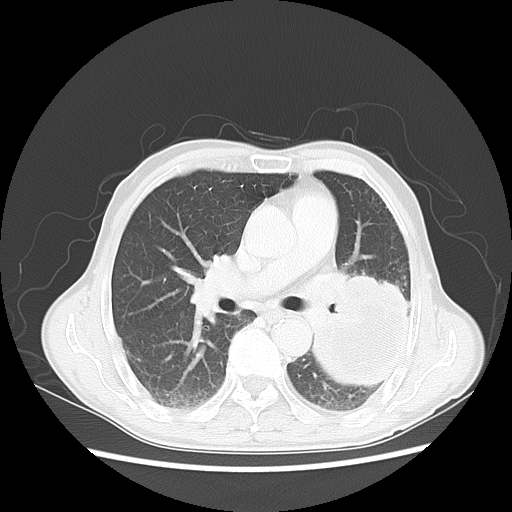
Chest CT, one axial slice; position 29 of 51 along the scan axis; reconstruction kernel LUNG; lung window (W 1500 / L -600 HU); 5 mm slice thickness; 512 × 512 image matrix. Male patient, age 64 years. From the clinical record (not read from this slice): clinical TNM (as recorded): T4 N0 M0; histopathological grade: G2-3.
Annotated regions visible in this slice (bounding box drawn by a radiologist):
- lung tumour (recorded histology: squamous cell carcinoma): box from (x=316, y=276) to (x=413, y=384) px